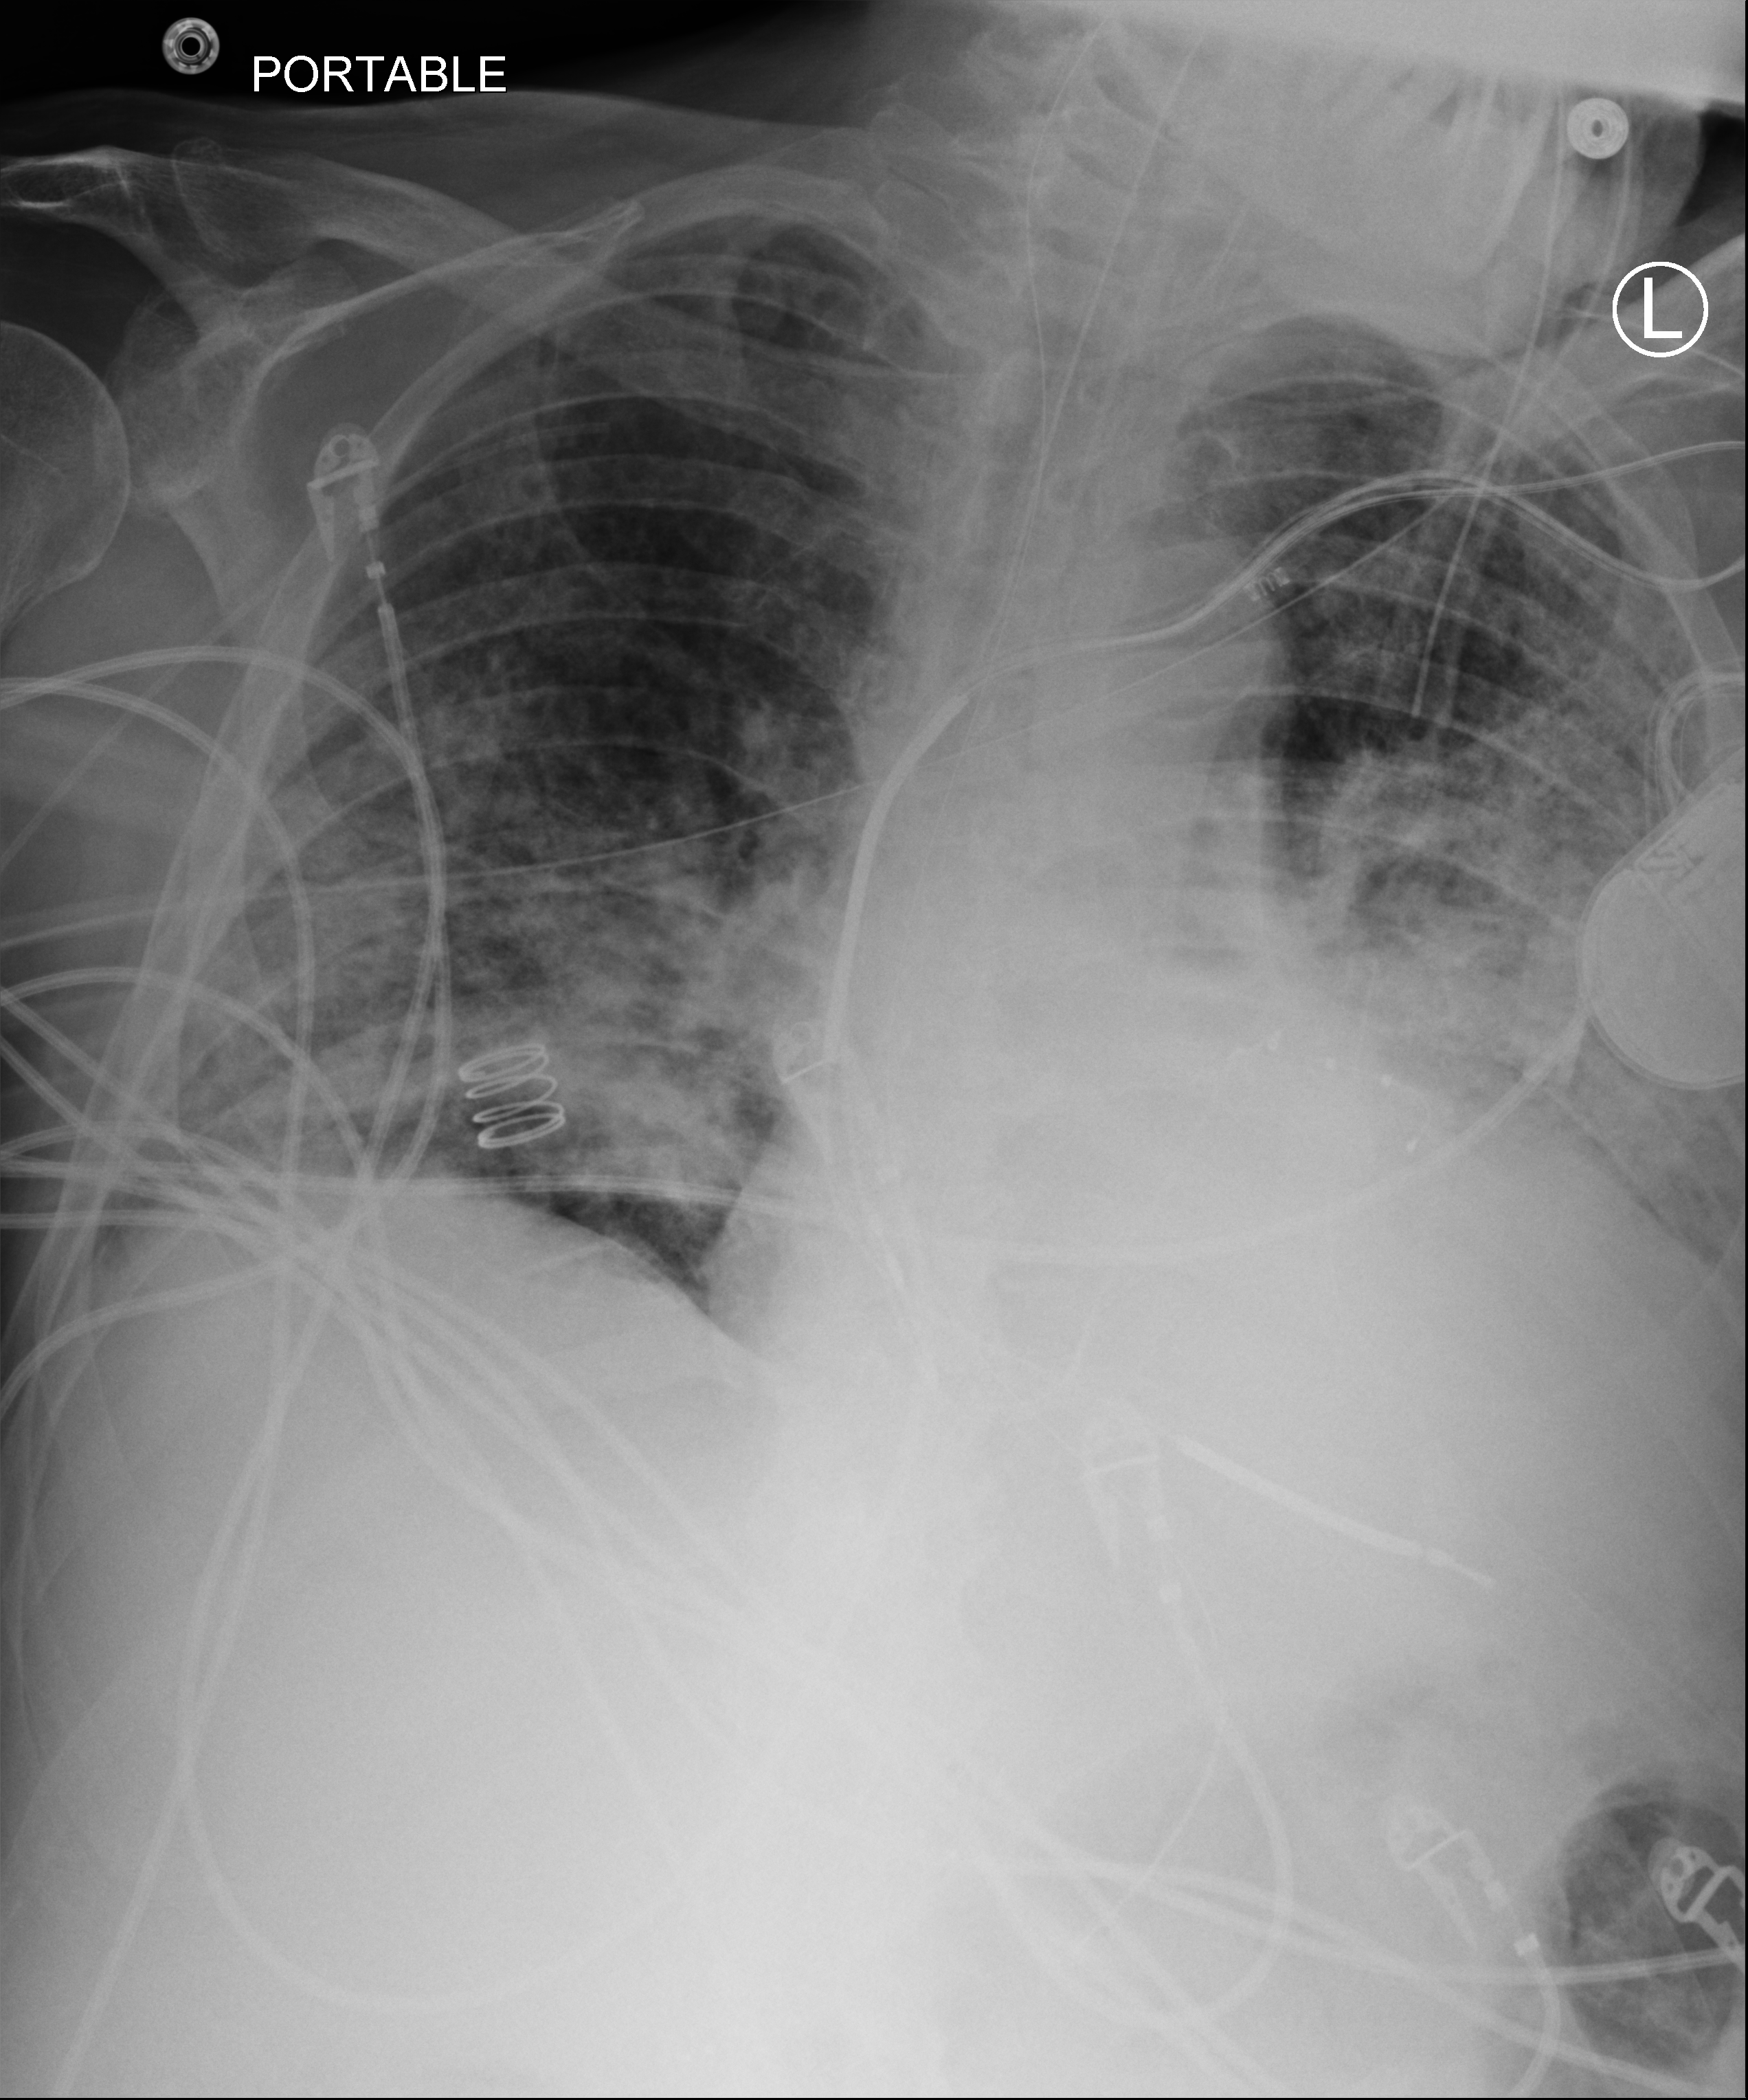
Portable chest radiograph, anteroposterior (AP) projection. Male patient hospitalised with COVID-19, age 60–74 years.
Admission-level facts for this patient (not findings on this image; timing relative to this image not recorded): mechanically ventilated during this hospital stay: yes; admitted to intensive care during this hospital stay: yes; length of hospital stay: 36 days.